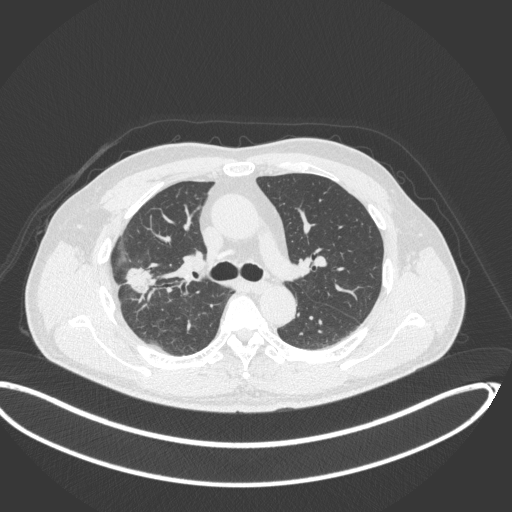
Chest CT, one axial slice; position 222 of 341 along the scan axis; reconstruction kernel B31f; lung window (W 1500 / L -600 HU); 1 mm slice thickness; 512 × 512 image matrix. Male patient, age 63 years. From the clinical record (not read from this slice): clinical TNM (as recorded): T1c N0 M0; histopathological grade: G2-3.
Annotated regions visible in this slice (bounding box drawn by a radiologist):
- lung tumour (recorded histology: adenocarcinoma): box from (x=122, y=257) to (x=162, y=300) px